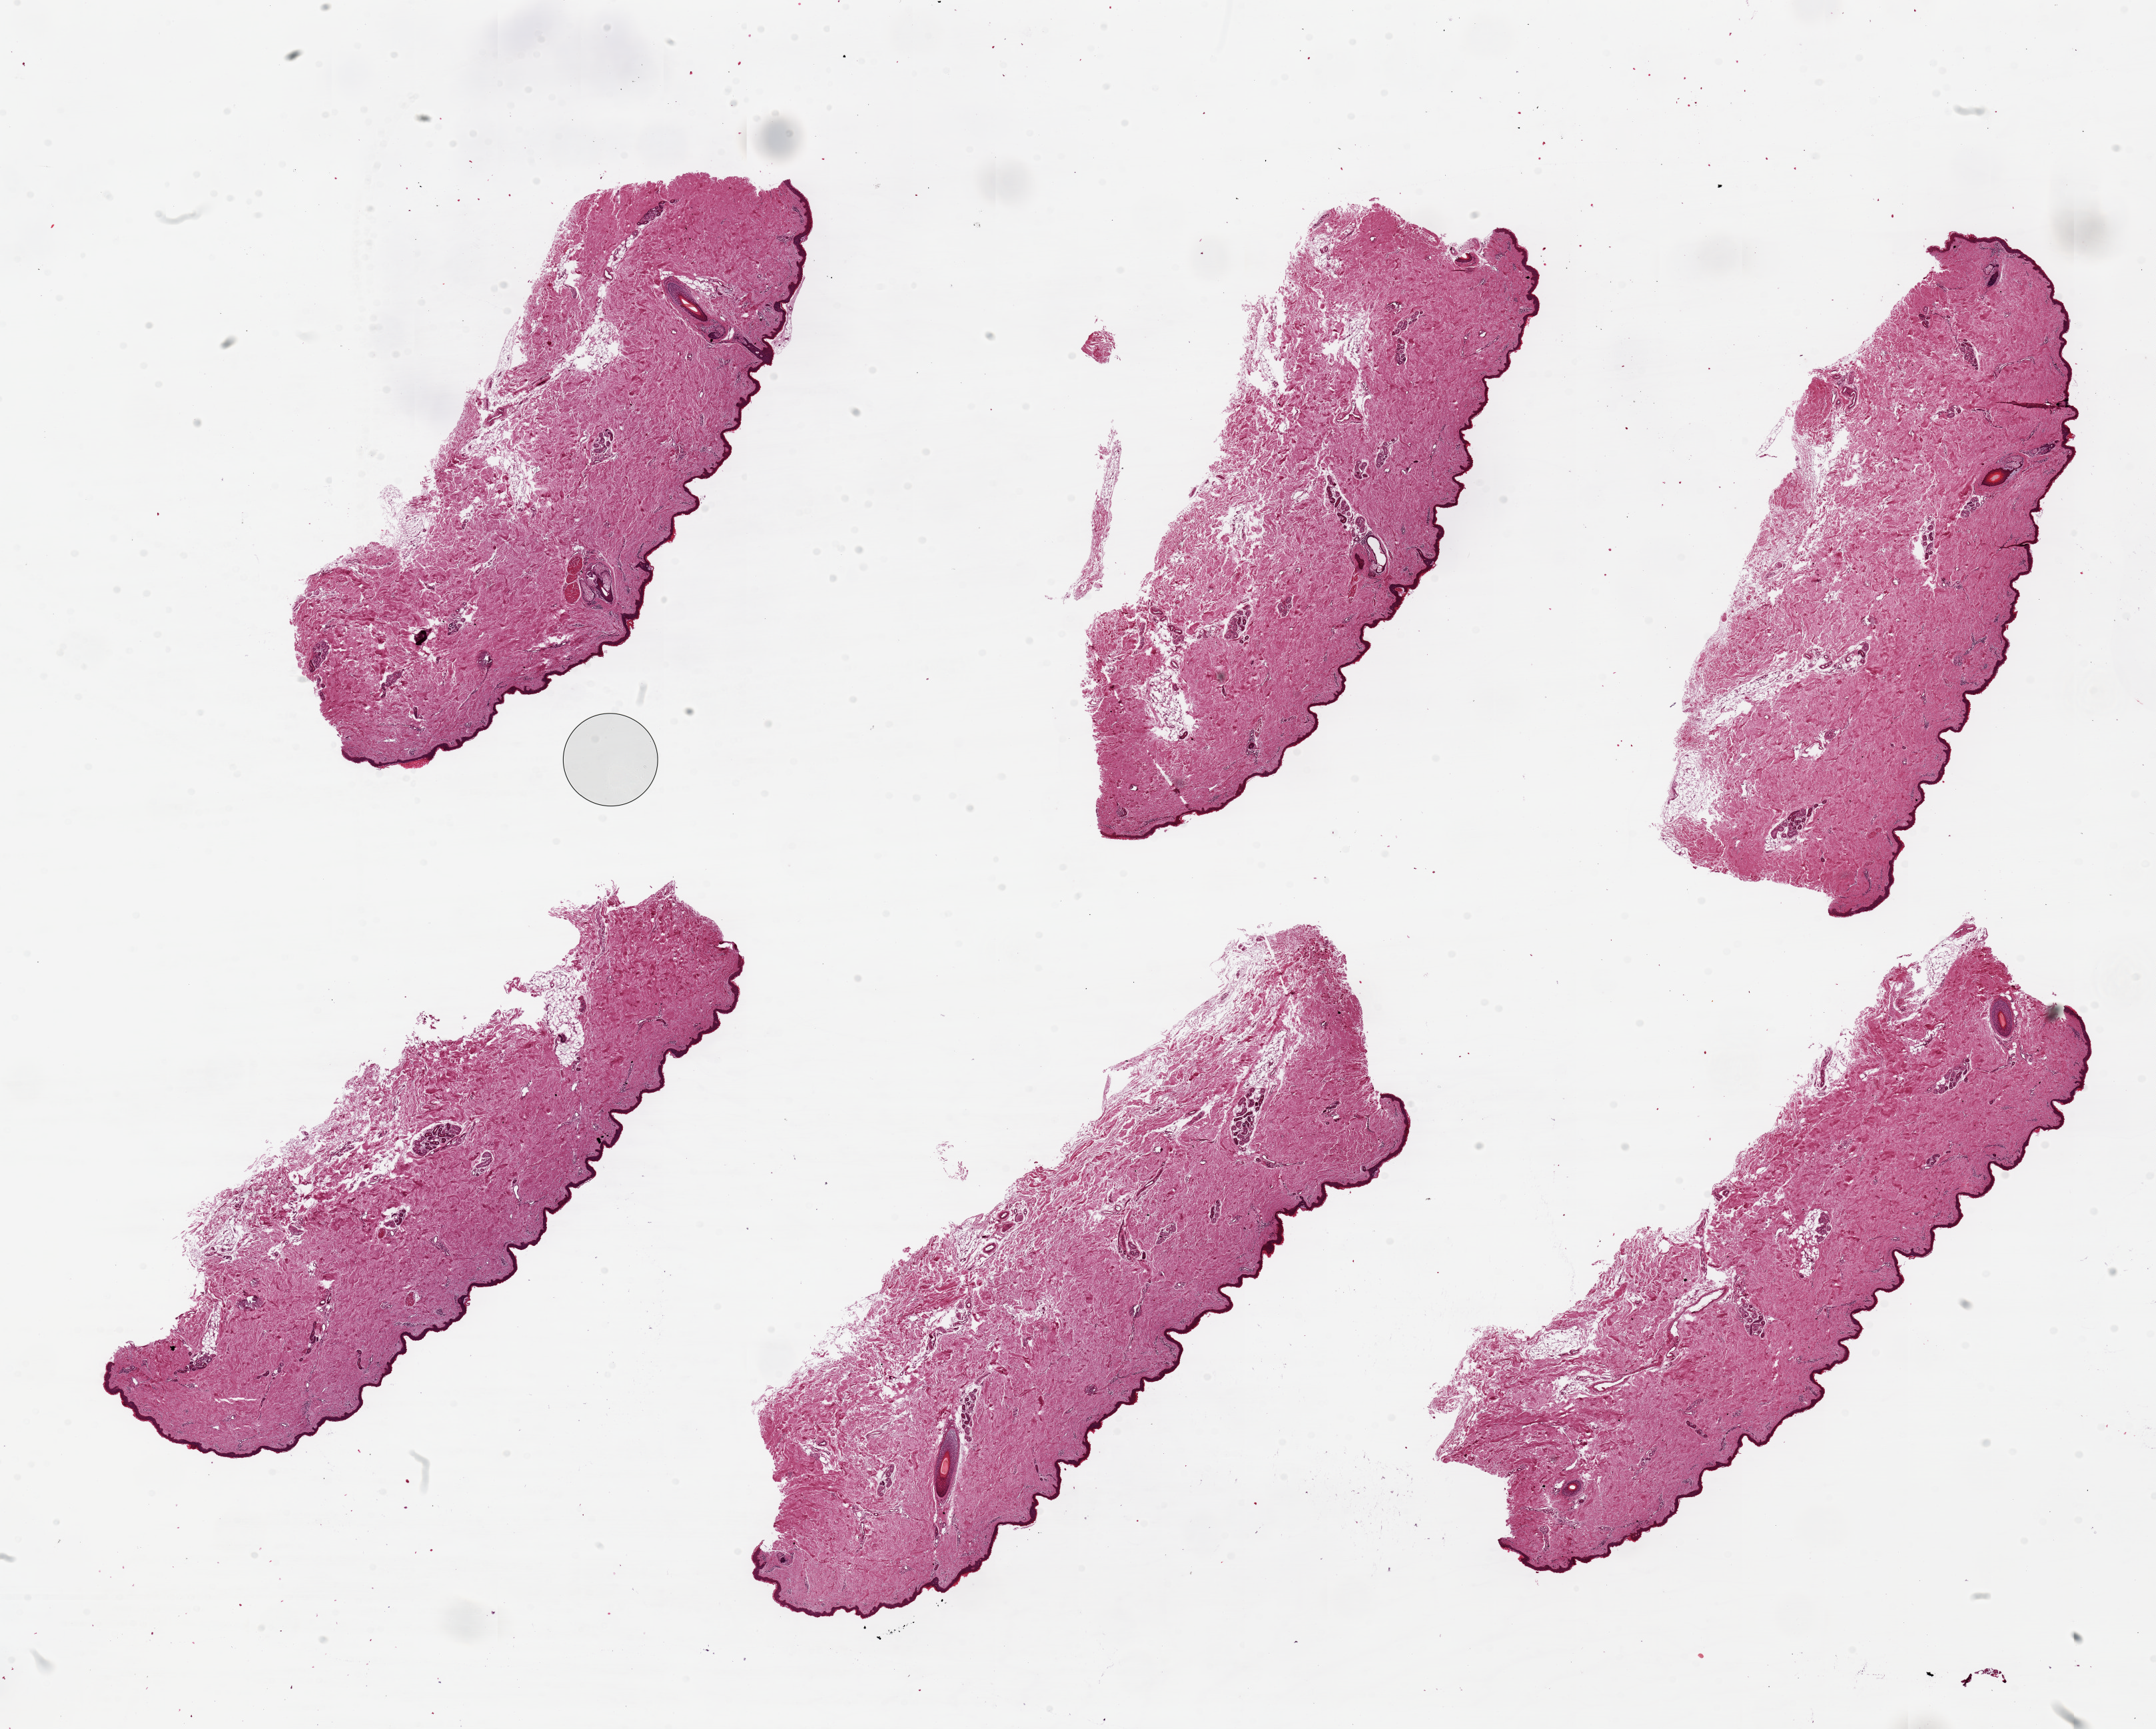
Digitized H&E-stained section, shown as a low-resolution overview of the whole scanned area (about 25.6 x 20.5 mm), PAXgene-fixed paraffin-embedded (PFPE) section, sampled site (target tissue): skin of lower leg, donor tissue sample. Donor sex: male.
• reviewer comment on this tissue sample: 6 pieces, up to 9.6x3 mm; well cleaned of subcutaneous adipose